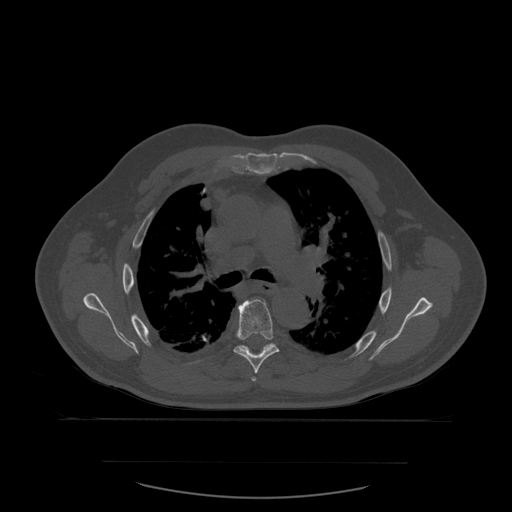
CT including the spine, one axial slice; position 403 of 590 along the scan axis; bone window (W 1800 / L 400 HU); 512 × 512 image matrix. Patient age 71 years. Case-level facts recorded for this patient, not image findings: primary cancer: lung; vertebrae with lytic lesions (as recorded): T1, T2, L5, S1.
Outlined on this slice (semi-automatically segmented with operator editing):
- T5 vertebra: box from (x=252, y=377) to (x=257, y=382) px
- T6 vertebra: (x=234, y=300)–(x=280, y=374)
- T7 vertebra: (x=238, y=343)–(x=276, y=353)